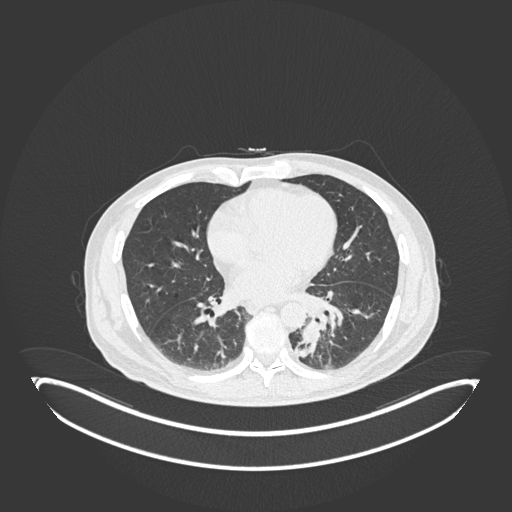
Chest CT, one axial slice. Slice 70 of 251 in the series (ordered by position). 120 kVp. Lung window (W 1500 / L -600 HU). 1 mm slice thickness. 512 × 512 image matrix, field of view 500 × 500 mm. Male patient, age 72 years. Case-level facts recorded for this patient, not image findings: clinical TNM (as recorded): T2b N0 M1.
Outlined on this slice (rectangle marked by the reading radiologist):
- lung tumour (recorded histology: adenocarcinoma): box from (x=296, y=317) to (x=320, y=359) px